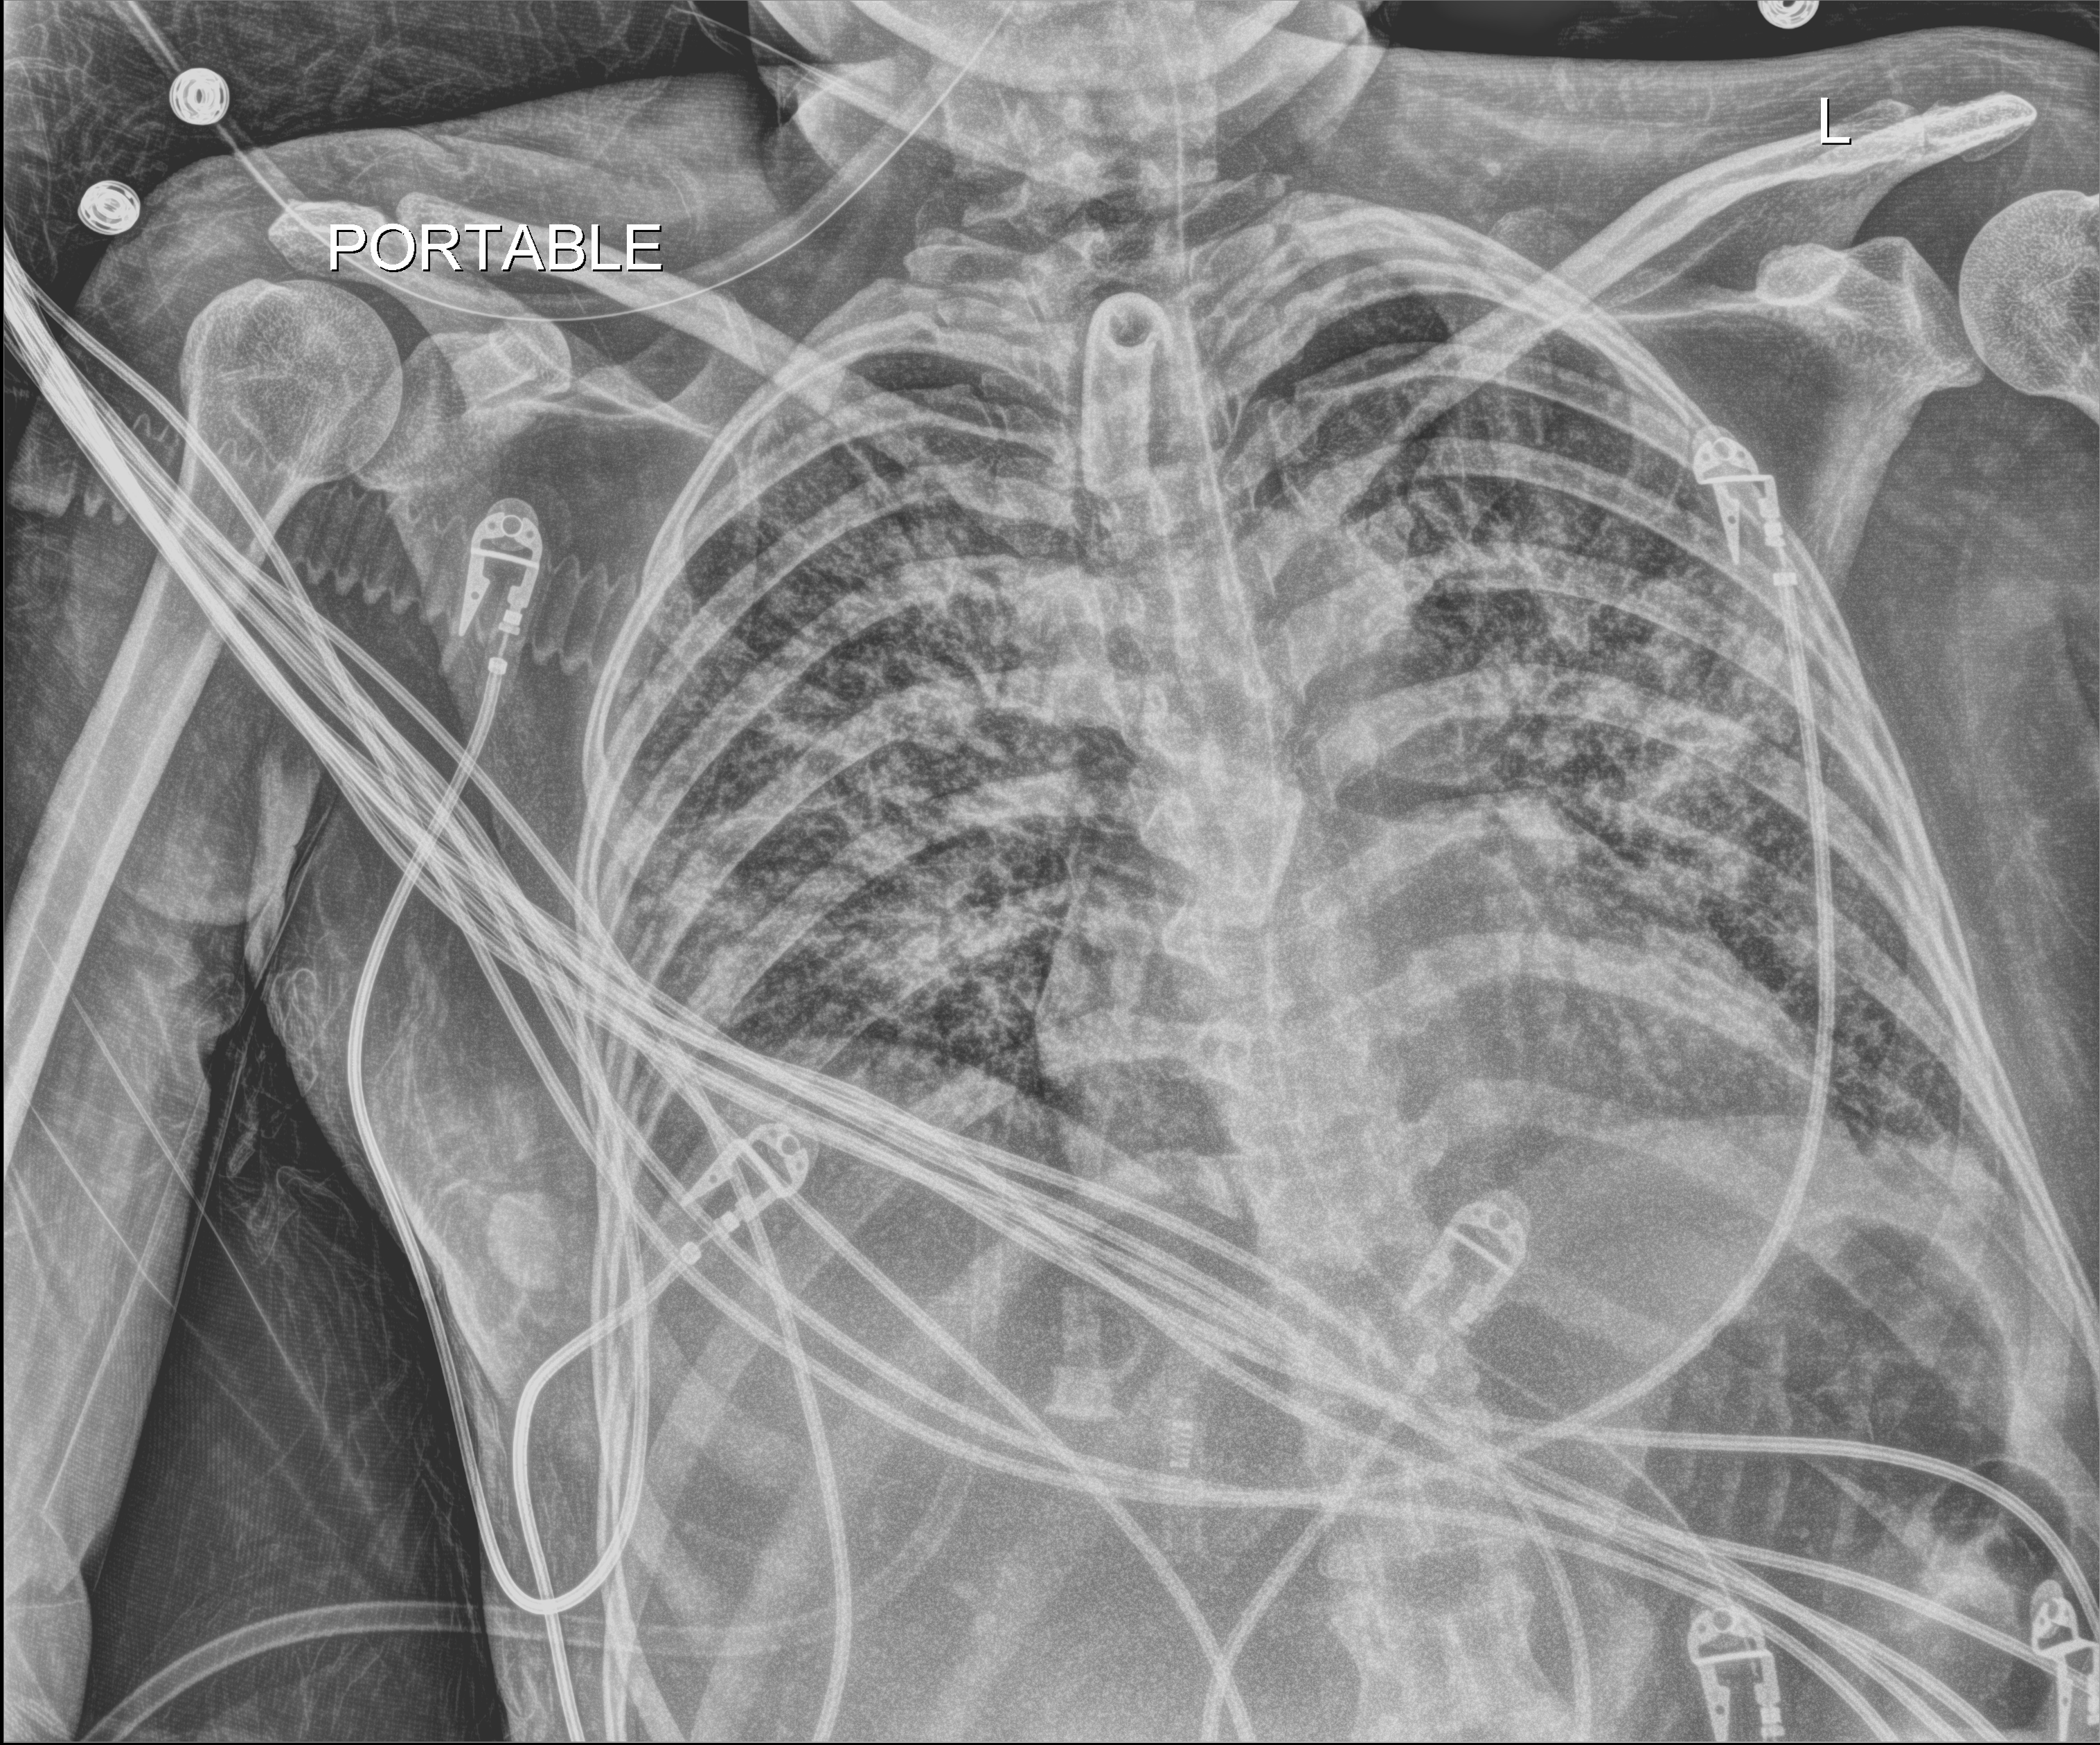
Chest X-ray (portable); anteroposterior (AP) projection. Patient hospitalised with COVID-19; female, aged 18–59 years.
From the hospital-stay record, not from the radiograph (when in the stay this image was taken is not recorded):
- admitted to intensive care during this hospital stay: yes
- diabetes (admission record): no
- mechanically ventilated during this hospital stay: yes